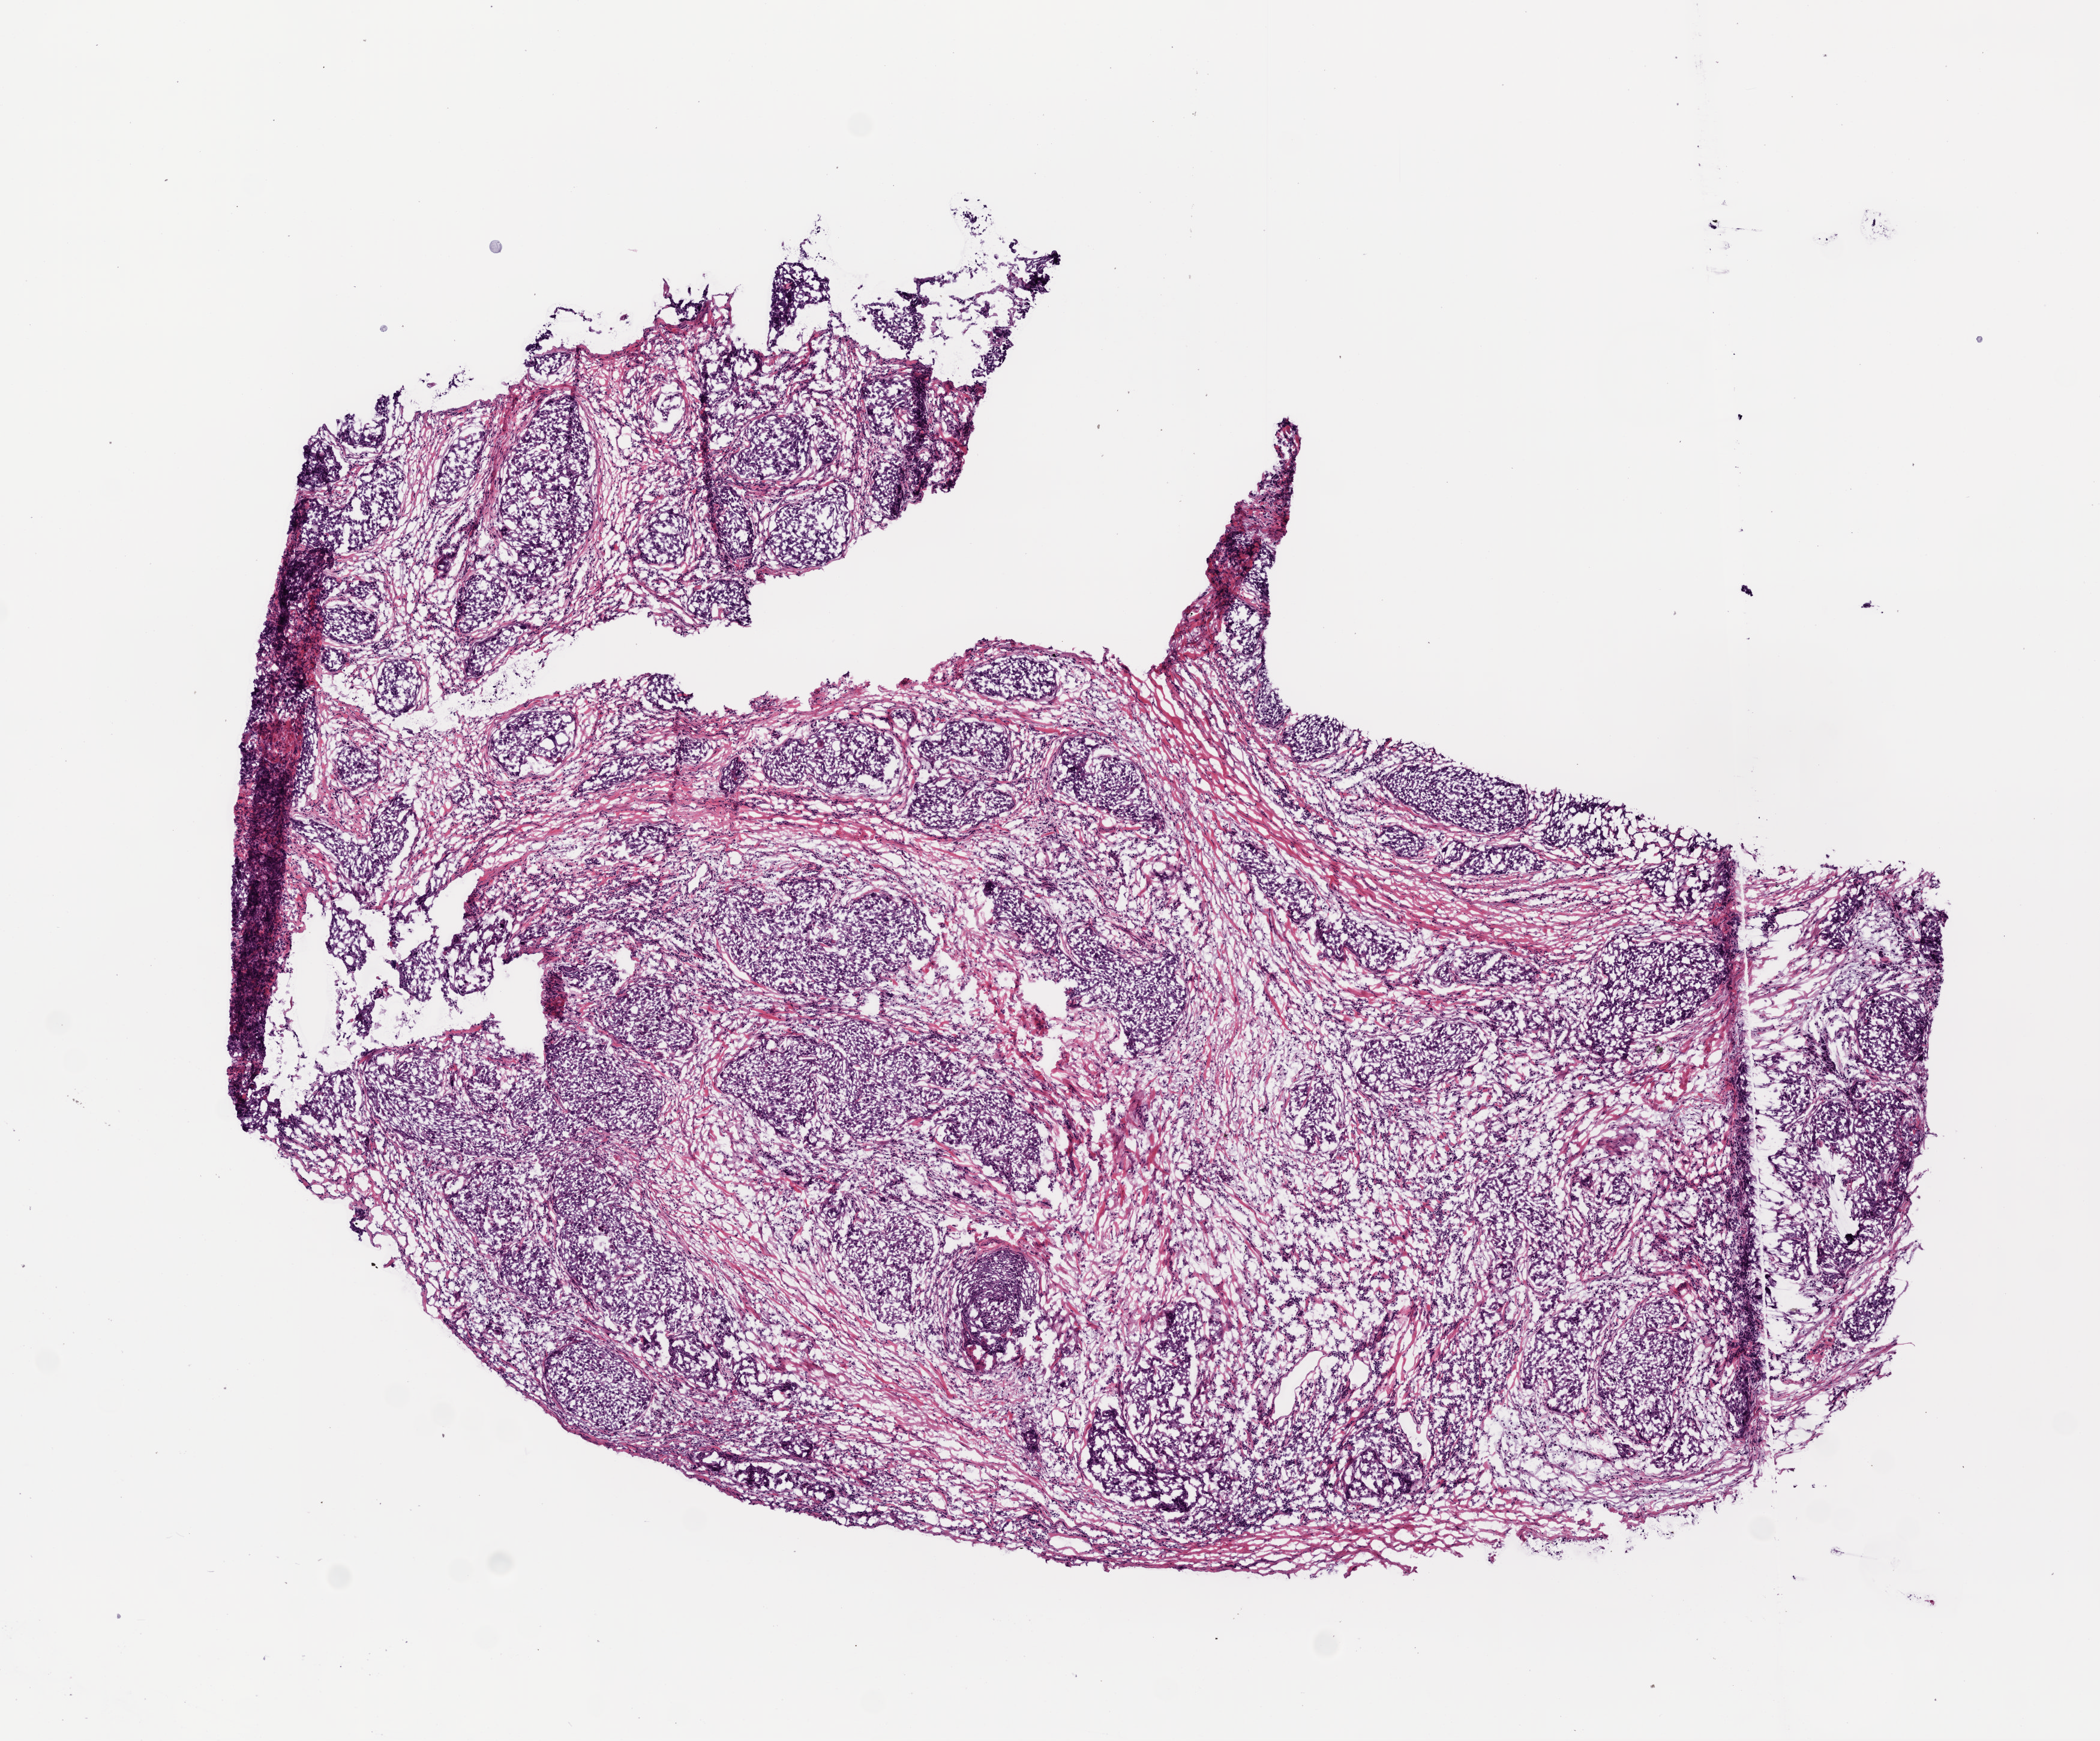
Whole-slide histology image, H&E — whole scanned area (about 7.0 x 5.8 mm, from a 20x scan) shown as a low-resolution overview; frozen section; head and neck, primary tumour sample. Male, age 61 years at initial diagnosis. Histologic grade: G3 (poorly differentiated). Pathologist review of this section (percent, as recorded): tumour cells 60%, tumour nuclei 50%, normal cells 0%, stromal cells 40%, necrosis 0%.
- TNM: T4a N2a
- AJCC pathologic stage: IVA (7th edition)
- pathologic diagnosis: Squamous cell carcinoma, NOS (larynx, NOS)